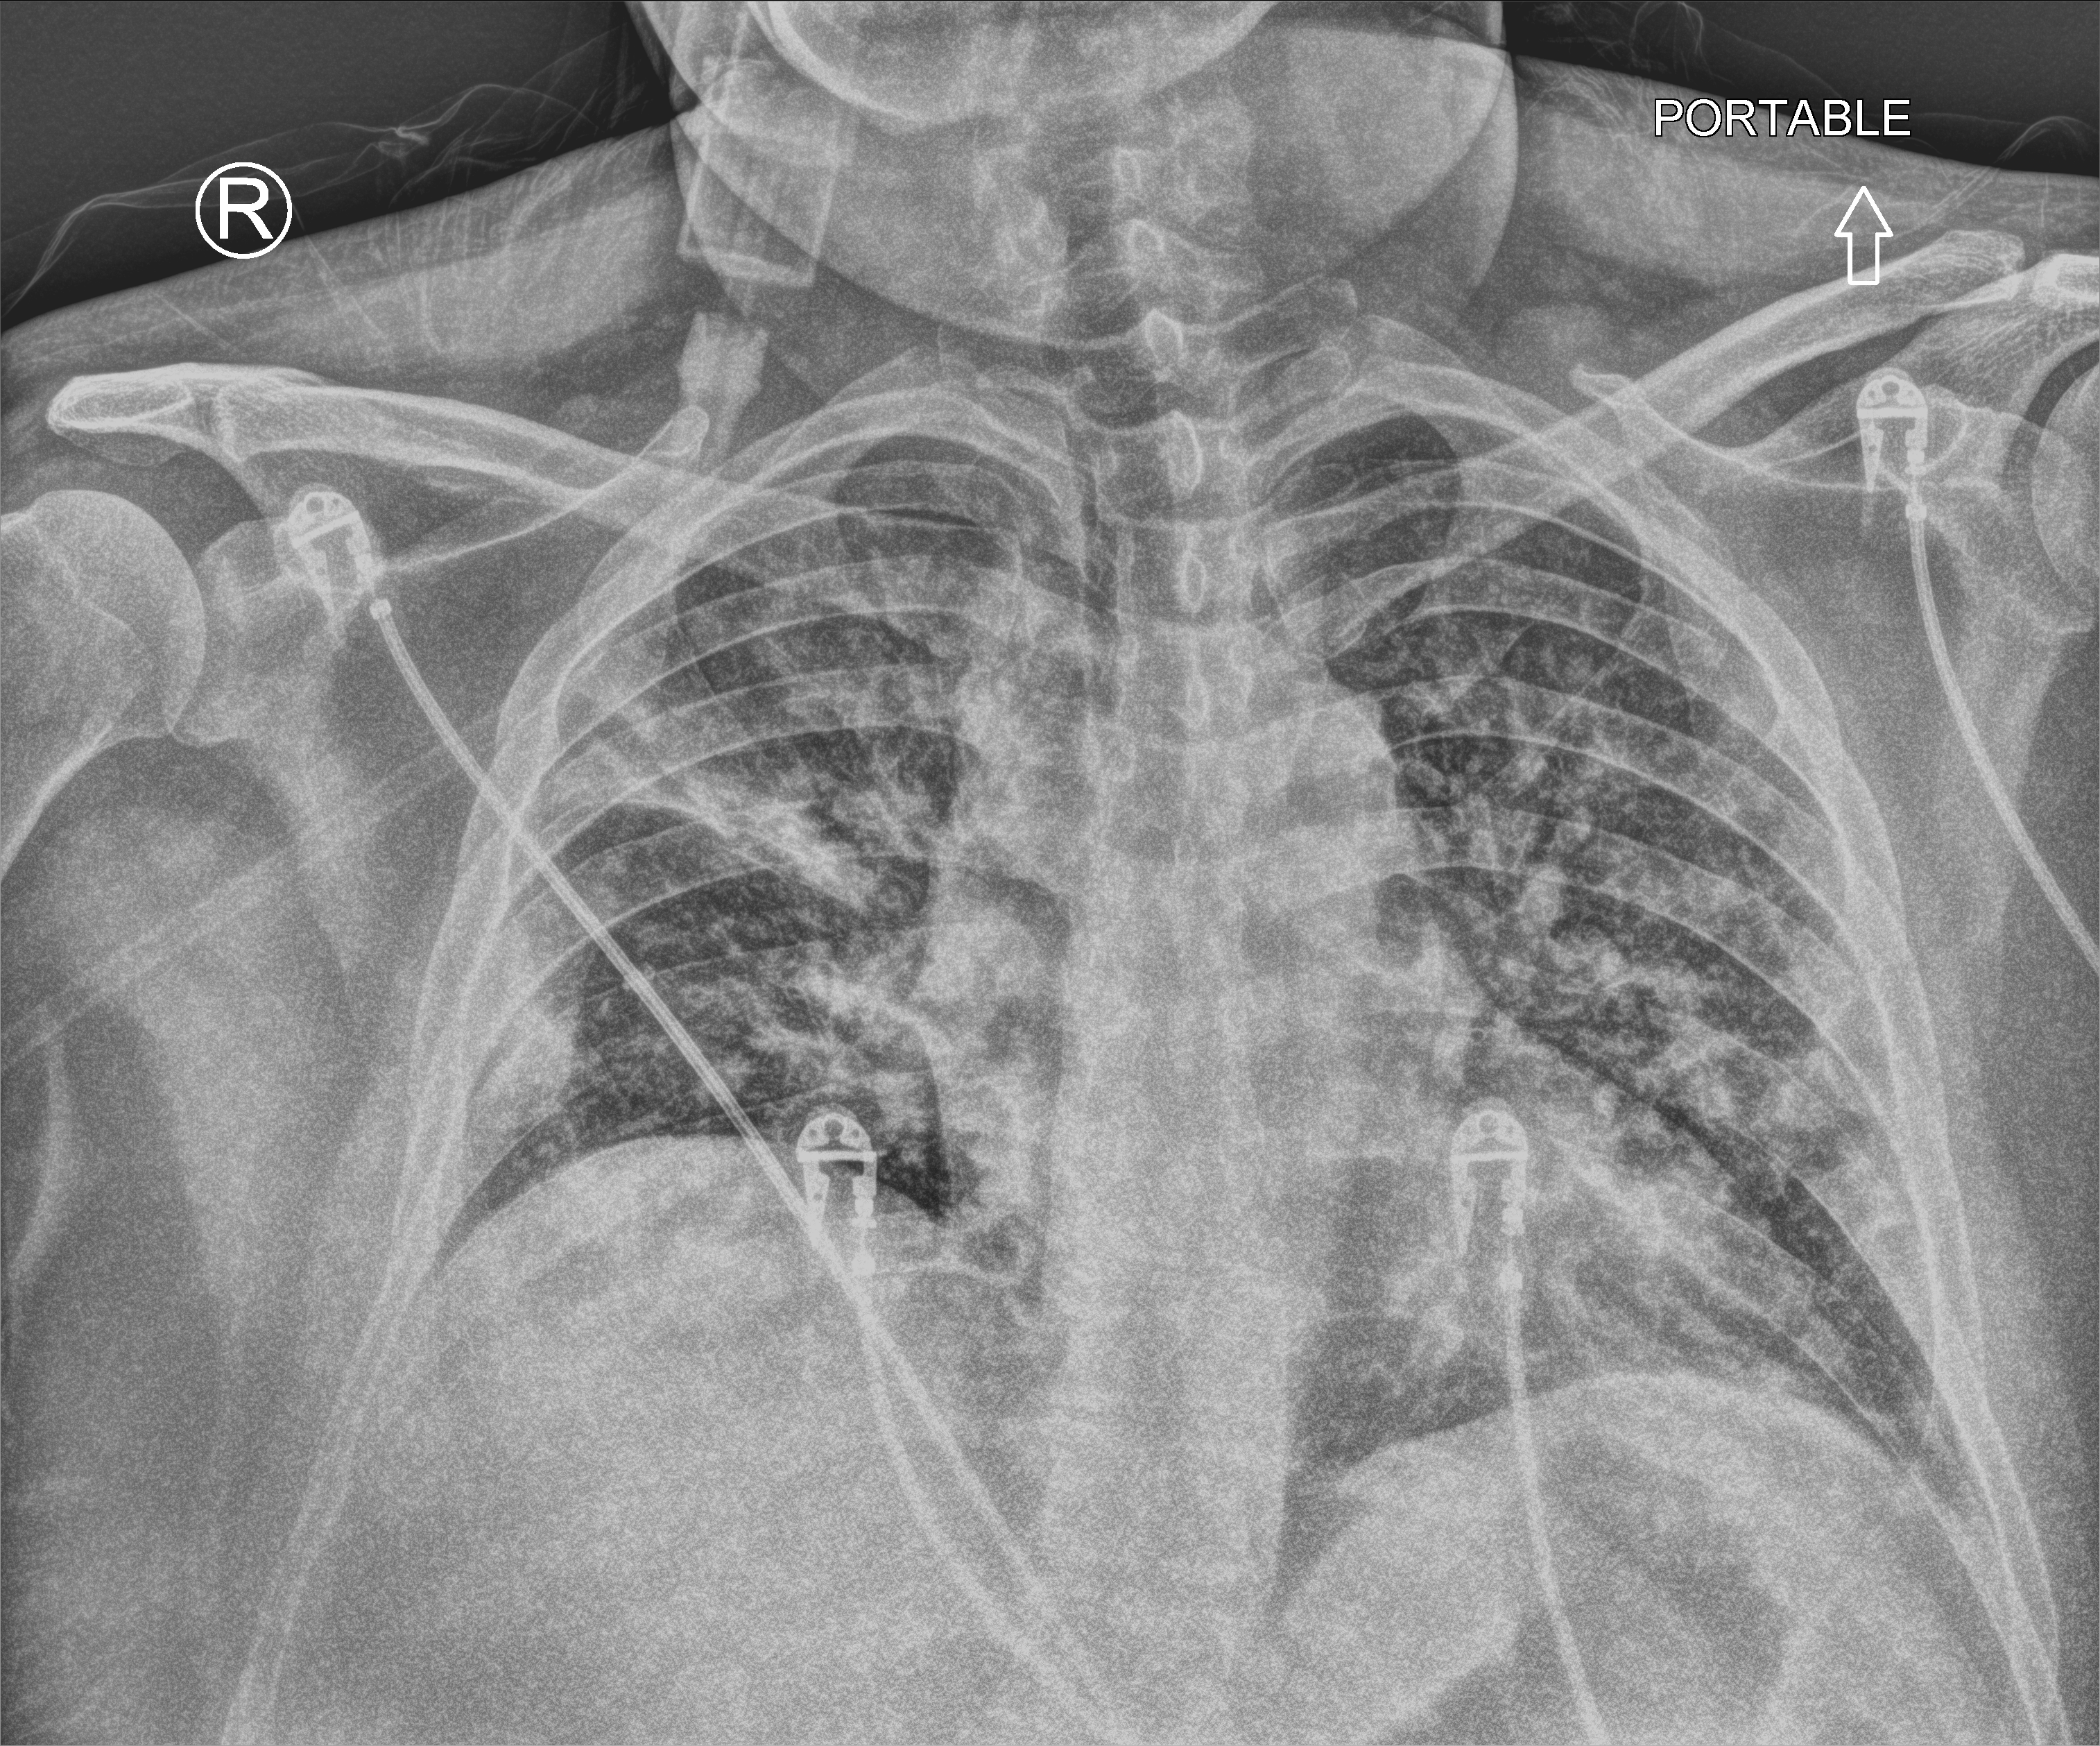
Chest X-ray (portable), anteroposterior (AP) projection. Patient hospitalised with COVID-19; male, aged 18–59 years.
From the hospital-stay record, not from the radiograph (when in the stay this image was taken is not recorded): length of hospital stay: 63 days; mechanically ventilated during this hospital stay: yes.